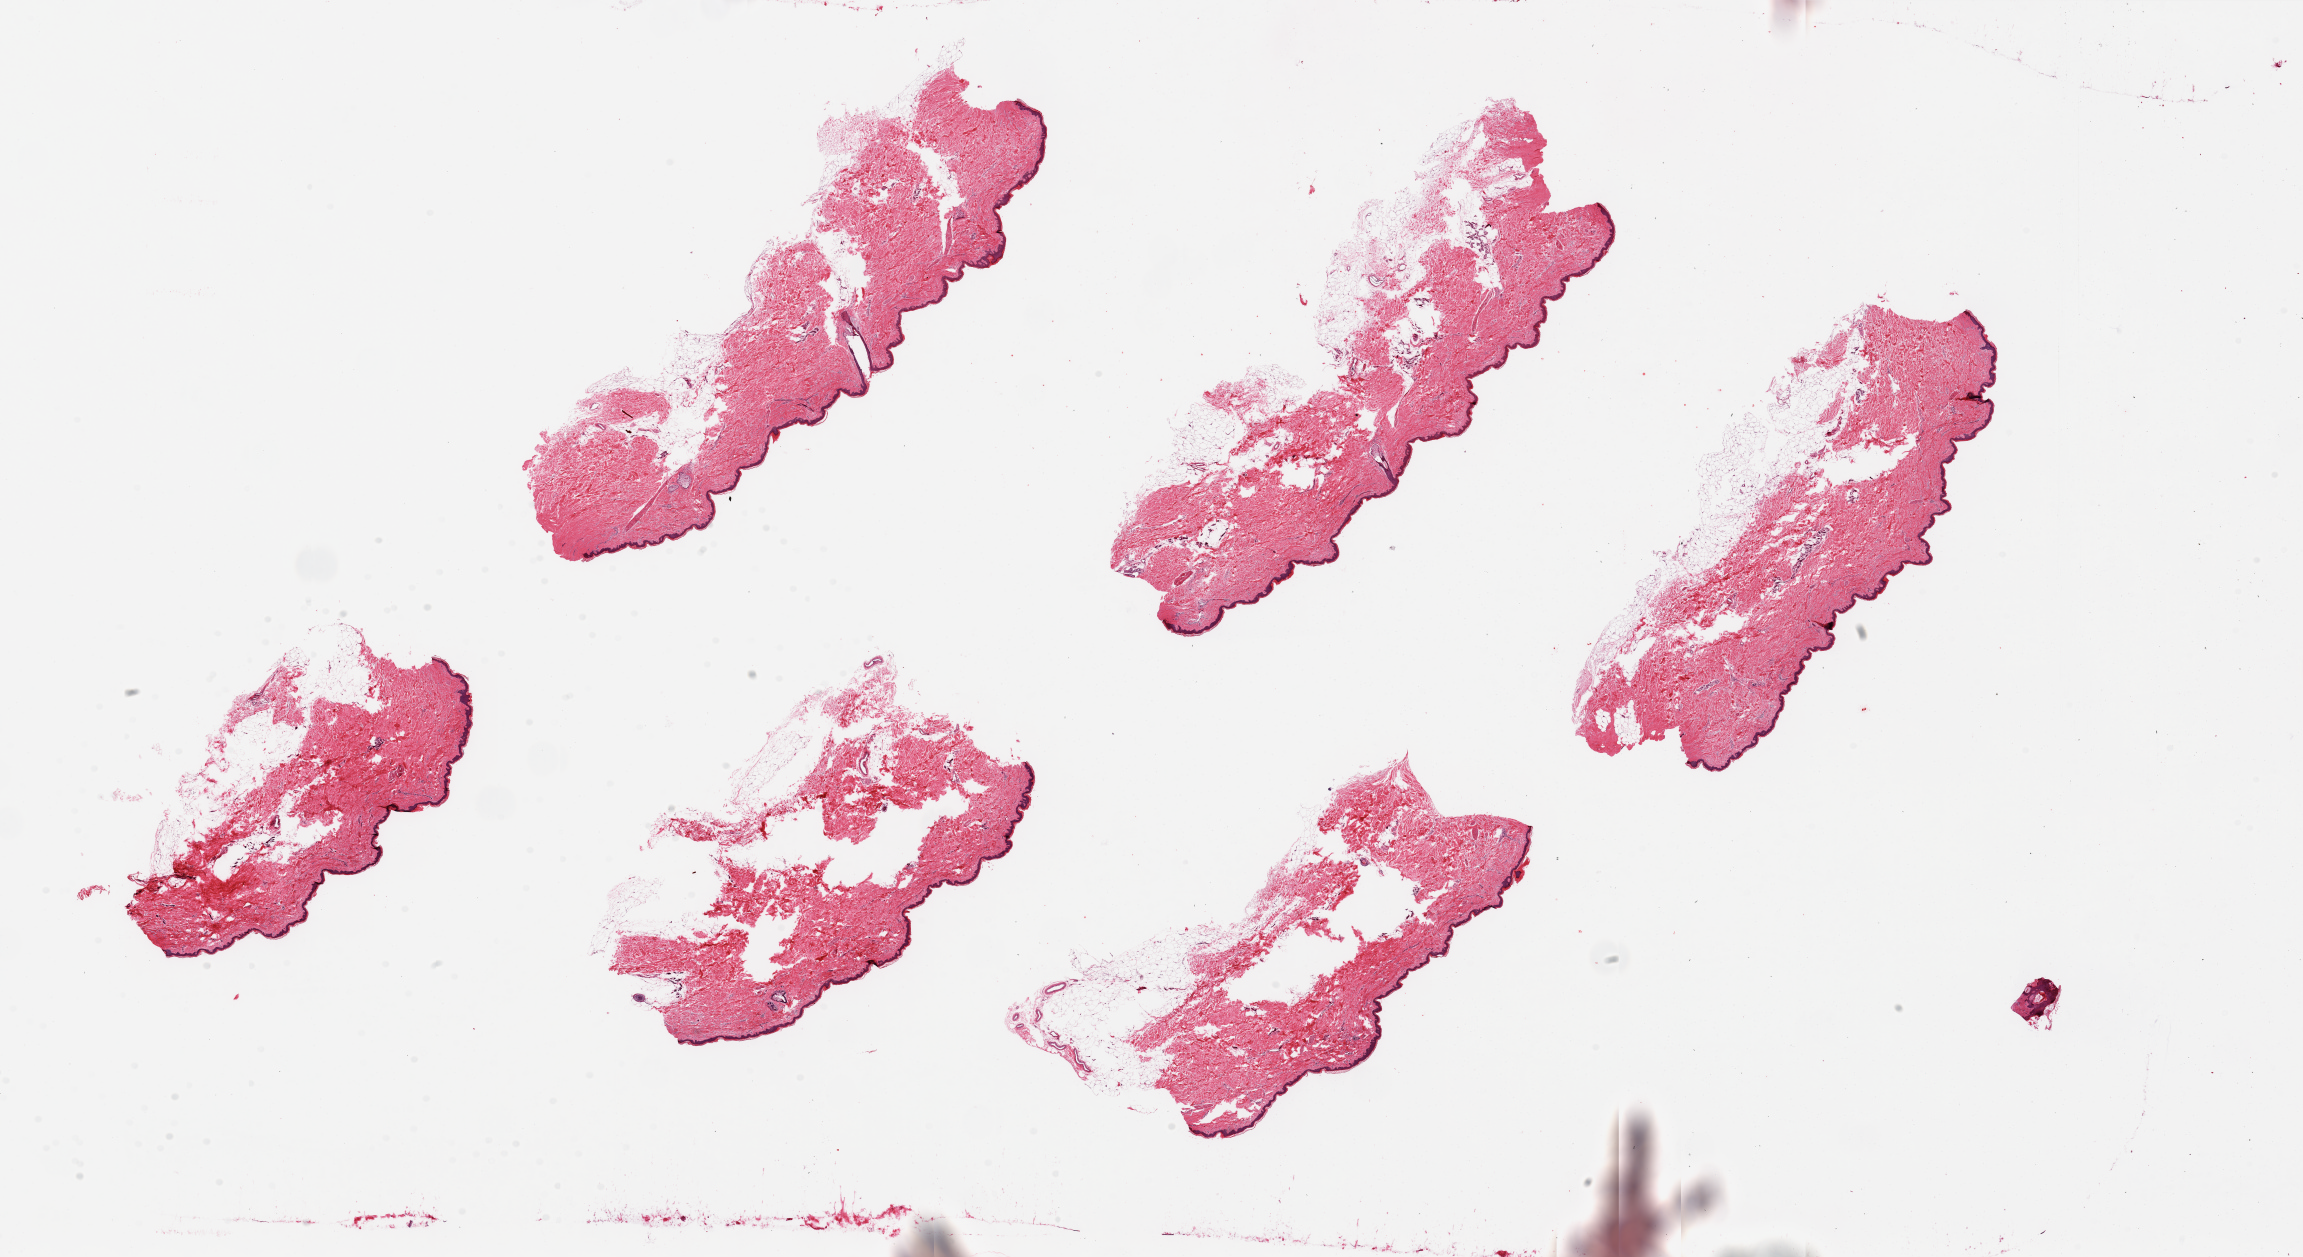
Digitized H&E-stained section — whole scanned area (about 36.4 x 19.9 mm) shown as a low-resolution overview. PAXgene-fixed, paraffin-embedded tissue. Section of skin of lower leg (target tissue). Donor tissue sample. Donor sex: female.
* pathologist's review note for this sample: 6 pieces, up to 10x3.5mm; up to 0.7mm subcutaneous adipose